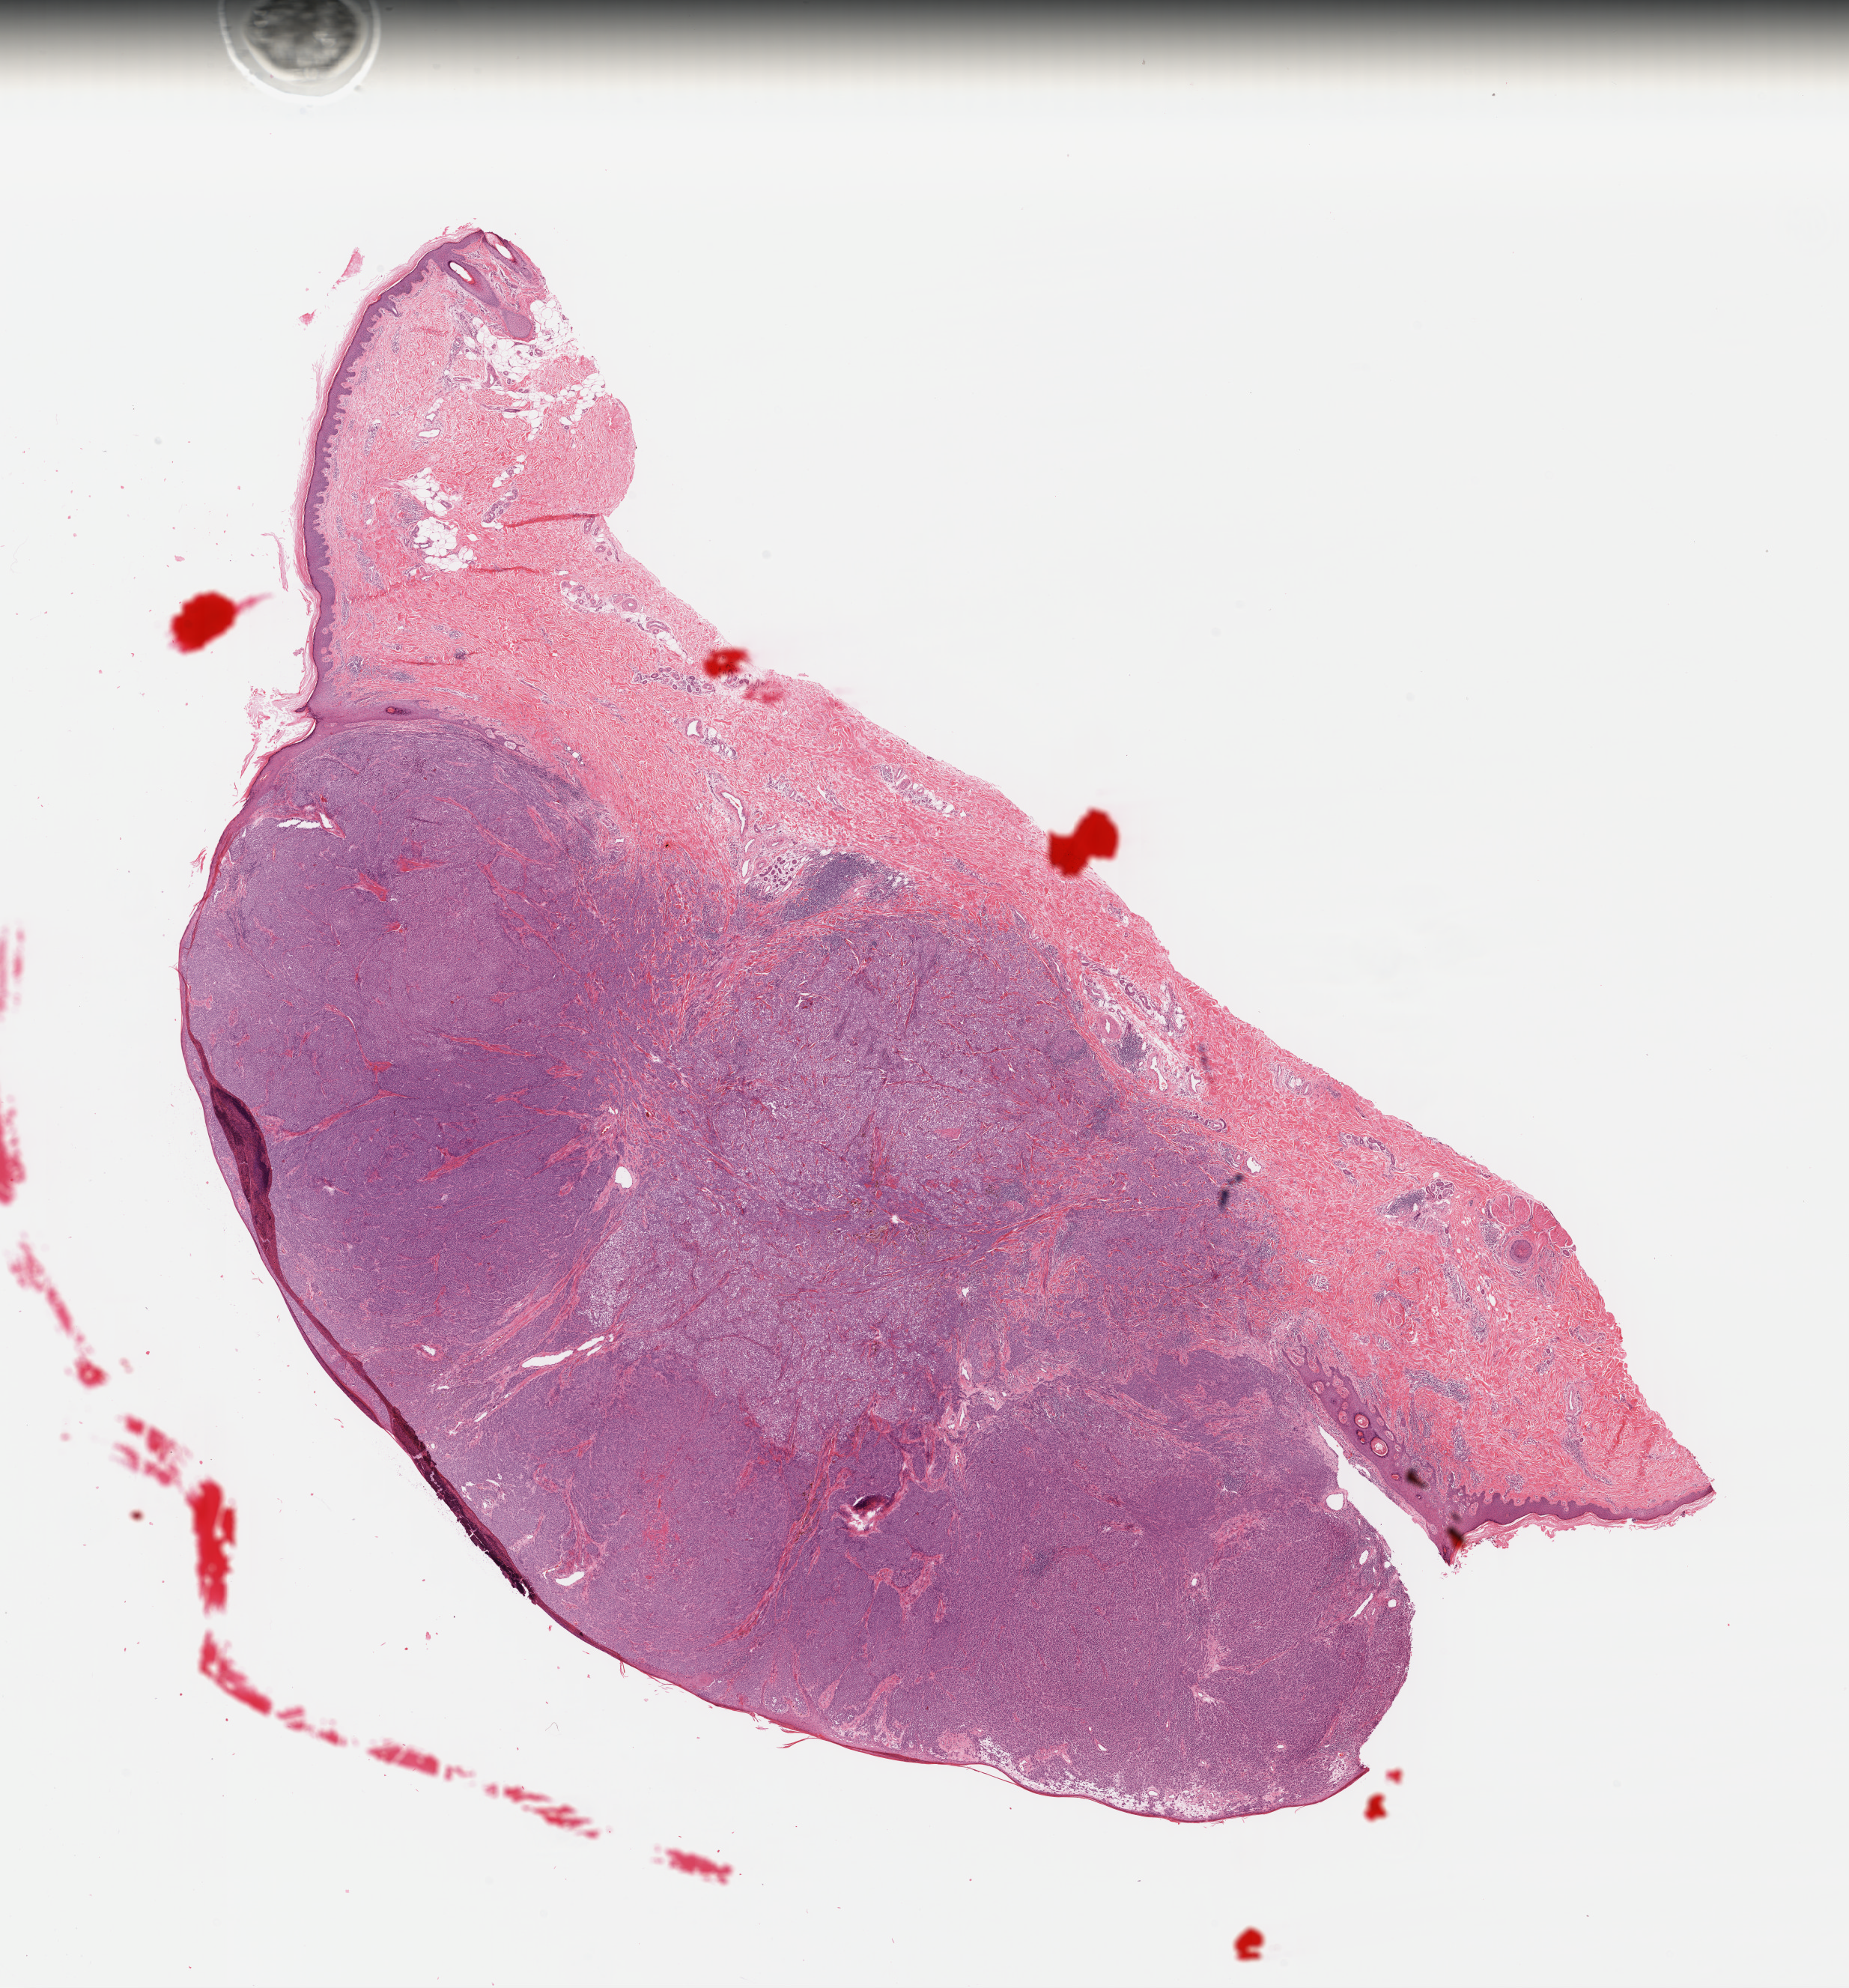
H&E whole-slide image, low-resolution overview of the scanned area, about 19.4 x 20.9 mm (from a 40x scan), formalin-fixed paraffin-embedded (FFPE) diagnostic section, skin, primary tumour sample. Female, age 56 years at initial diagnosis.
Histologic diagnosis: Nodular melanoma. TNM: T4b NX M0. AJCC pathologic stage: IIC (7th edition).